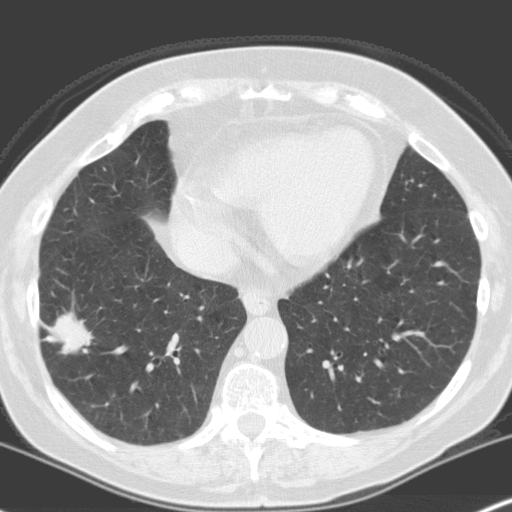
Axial slice from a low-dose chest CT screening exam; baseline screening round; lung window (W 1500 / L -600 HU); 512 × 512 image matrix, field of view 316 × 316 mm. Female participant, aged 70 years at enrolment. Current smoker at enrolment.
• Lesion marked by an expert reader, bounding box <31,298,100,367> (left, top, right, bottom; pixels).
• The screening reader recorded 4 non-calcified nodules or masses ≥4 mm on this exam (right lower lobe, right upper lobe, left upper lobe, left upper lobe); which of them this box marks is not recorded.
• Official screen result: positive, change unspecified: nodule(s) >= 4 mm or enlarging nodule(s), mass(es), or other non-specific abnormalities suspicious for lung cancer.
• Later outcome: lung cancer diagnosed 28 days after this screen — adenocarcinoma, NOS, right lower lobe, moderately differentiated (G2), stage IV (AJCC 6th edition), 28 mm at pathology.